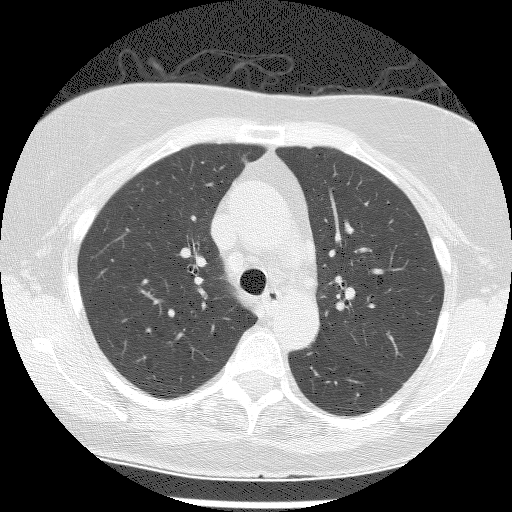
Low-dose screening chest CT, one axial slice; reconstruction kernel BONE; lung window (W 1500 / L -600 HU); 2.5 mm slice thickness; 512 × 512 image matrix, field of view 300 × 300 mm.
Structures marked on this image (outlined manually by an expert reader):
- lesion 1 (tumor, upper lobe of right lung): bounding box <242,155,250,167> (left, top, right, bottom; pixels)